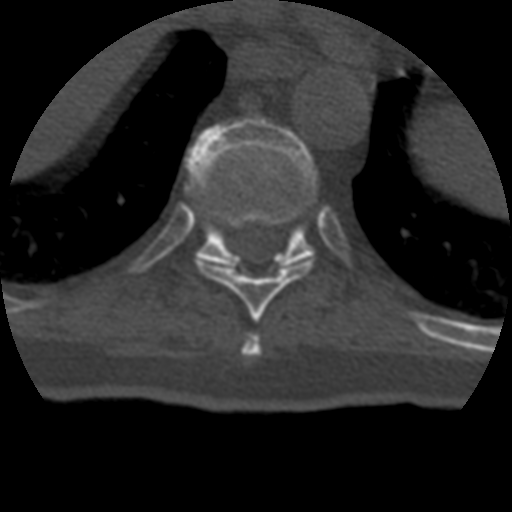
CT including the spine, one axial slice; position 231 of 399 along the scan axis; reconstruction kernel STANDARD; 120 kVp; bone window (W 1800 / L 400 HU); 512 × 512 image matrix, field of view 160 × 160 mm. Patient age 69 years. From the clinical record (not read from this slice): primary cancer: prostate.
Outlined on this slice (semi-automatically segmented with operator editing):
- T10 vertebra: bounding box <186,118,316,266> (left, top, right, bottom; pixels)
- T8 vertebra: <242,333,261,357>
- T9 vertebra: <200,205,311,319>